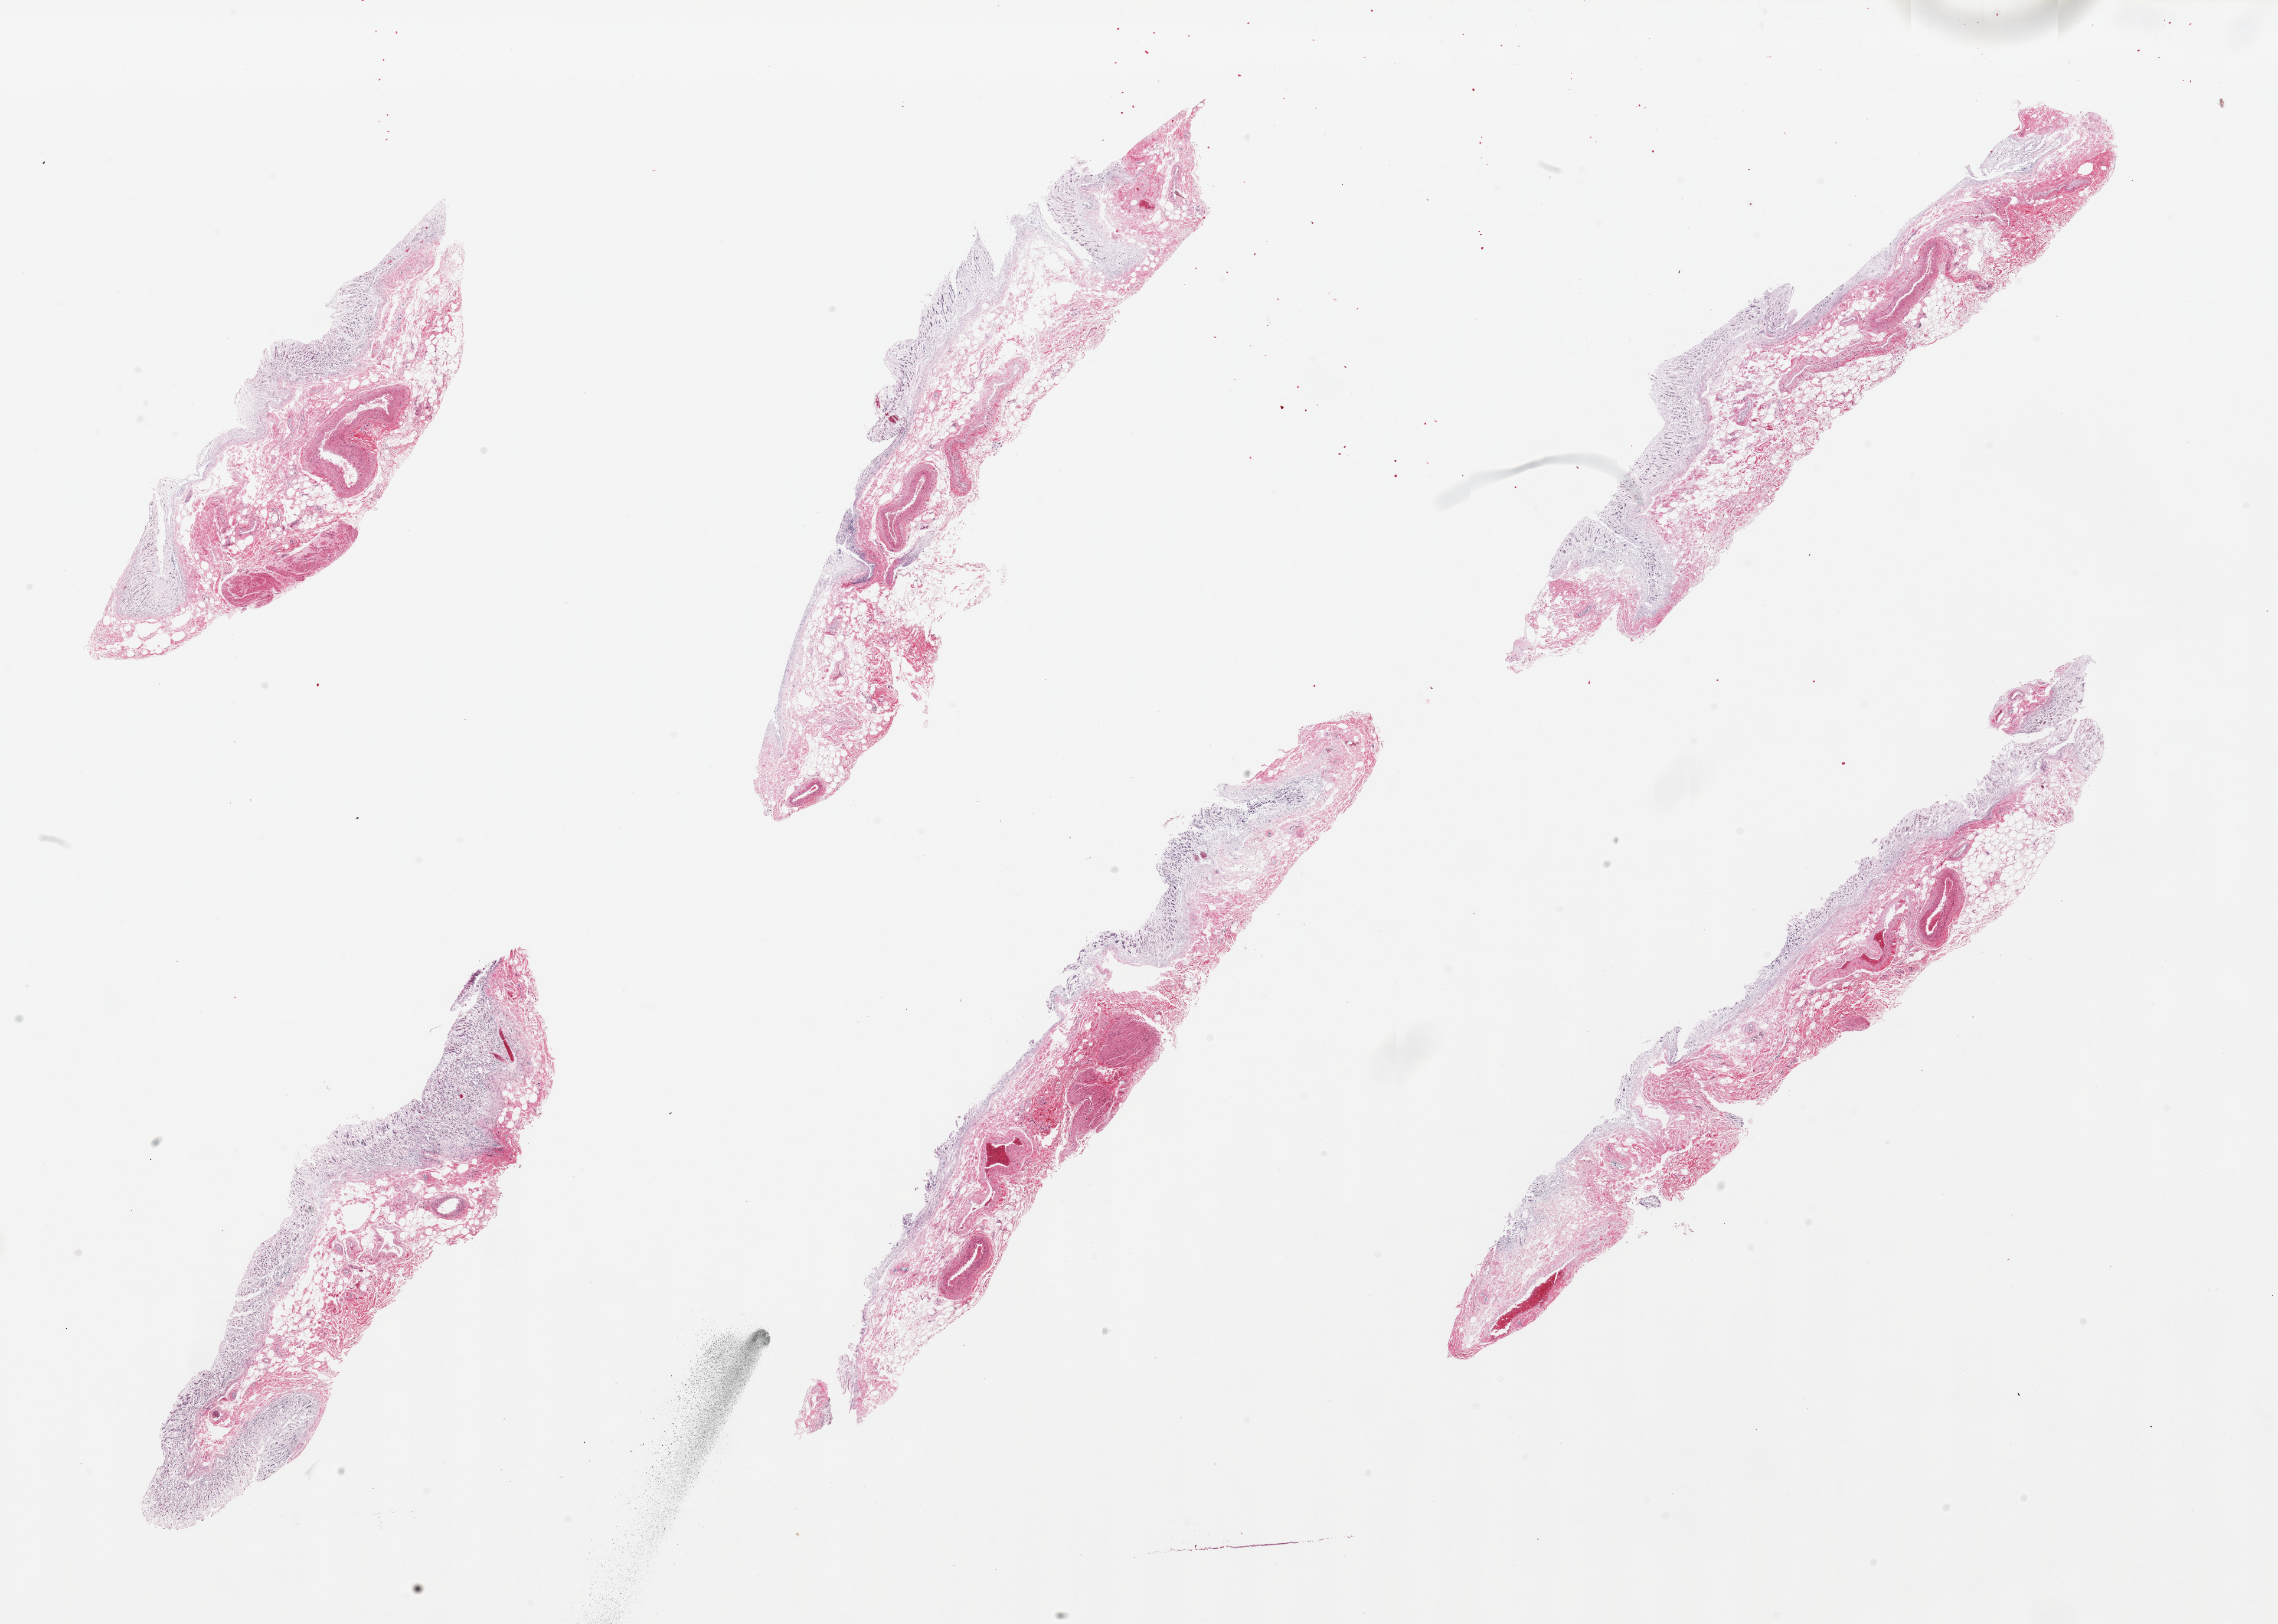
Digitized H&E-stained section — low-resolution overview of the scanned area, about 30.5 x 21.8 mm (acquisition: 20x scan); PAXgene-fixed, paraffin-embedded tissue; target tissue: stomach; tissue donor sample. Donor: male.
Pathologist's review note for this sample: 6 pieces, total autolysis of mucosa.